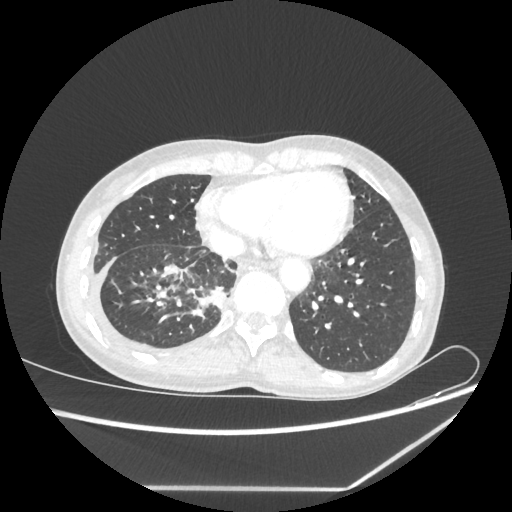
Chest CT, one axial slice. Position 72 of 237 along the scan axis. Reconstruction kernel STANDARD. Lung window (W 1500 / L -600 HU). 1.25 mm slice thickness. 512 × 512 image matrix, field of view 364 × 364 mm. Female patient, age 59 years. Case-level facts recorded for this patient, not image findings: clinical TNM (as recorded): T1c N1 M1.
Structures marked on this image (rectangle marked by the reading radiologist):
- lung tumour (recorded histology: adenocarcinoma): bounding box <209,286,227,310> (left, top, right, bottom; pixels)